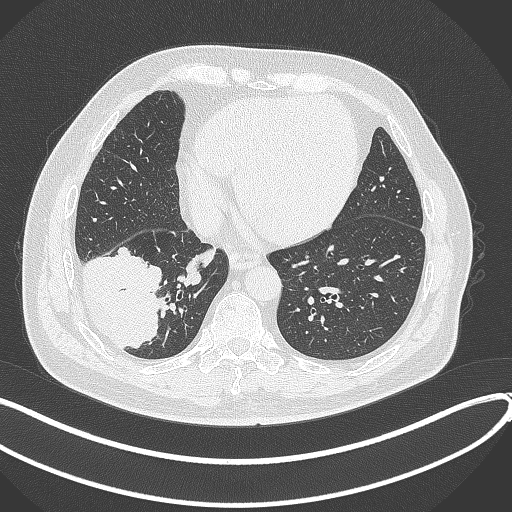
Chest CT, one axial slice. Slice 112 of 360 in the series (ordered by position). 120 kVp. Lung window (W 1500 / L -600 HU). 1 mm slice thickness. 512 × 512 image matrix, field of view 400 × 400 mm. Patient: male, 59 years.
Annotated regions visible in this slice (bounding box drawn by a radiologist):
- lung tumour (recorded histology: adenocarcinoma): bounding box <86,245,171,351> (left, top, right, bottom; pixels)